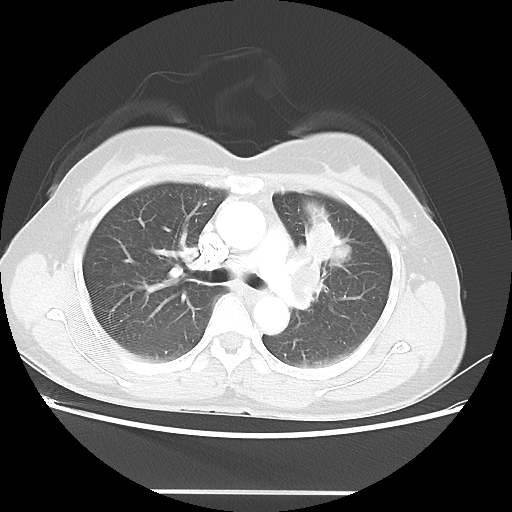
Chest CT, one axial slice. Position 29 of 46 along the scan axis. Reconstruction kernel LUNG. 100 kVp. Lung window (W 1500 / L -600 HU). 512 × 512 image matrix, field of view 360 × 360 mm. Female patient, age 50 years. From the clinical record (not read from this slice): clinical TNM (as recorded): T1c N1 M0; histopathological grade: G3.
Outlined on this slice (rectangle marked by the reading radiologist):
- lung tumour (recorded histology: adenocarcinoma): box from (x=297, y=199) to (x=354, y=271) px